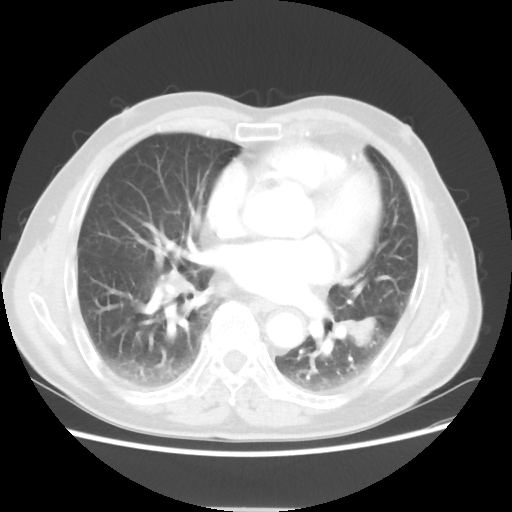
Chest CT, one axial slice; slice 32 of 64 in the series (ordered by position); reconstruction kernel STANDARD; lung window (W 1500 / L -600 HU); 512 × 512 image matrix. Male patient, age 71 years. Case-level facts recorded for this patient, not image findings: clinical TNM (as recorded): T1c N1 M0; histopathological grade: G2-3.
Structures marked on this image (bounding box drawn by a radiologist):
- lung tumour (recorded histology: adenocarcinoma): bounding box (x1, y1, x2, y2) in pixels: (340, 310, 378, 356)